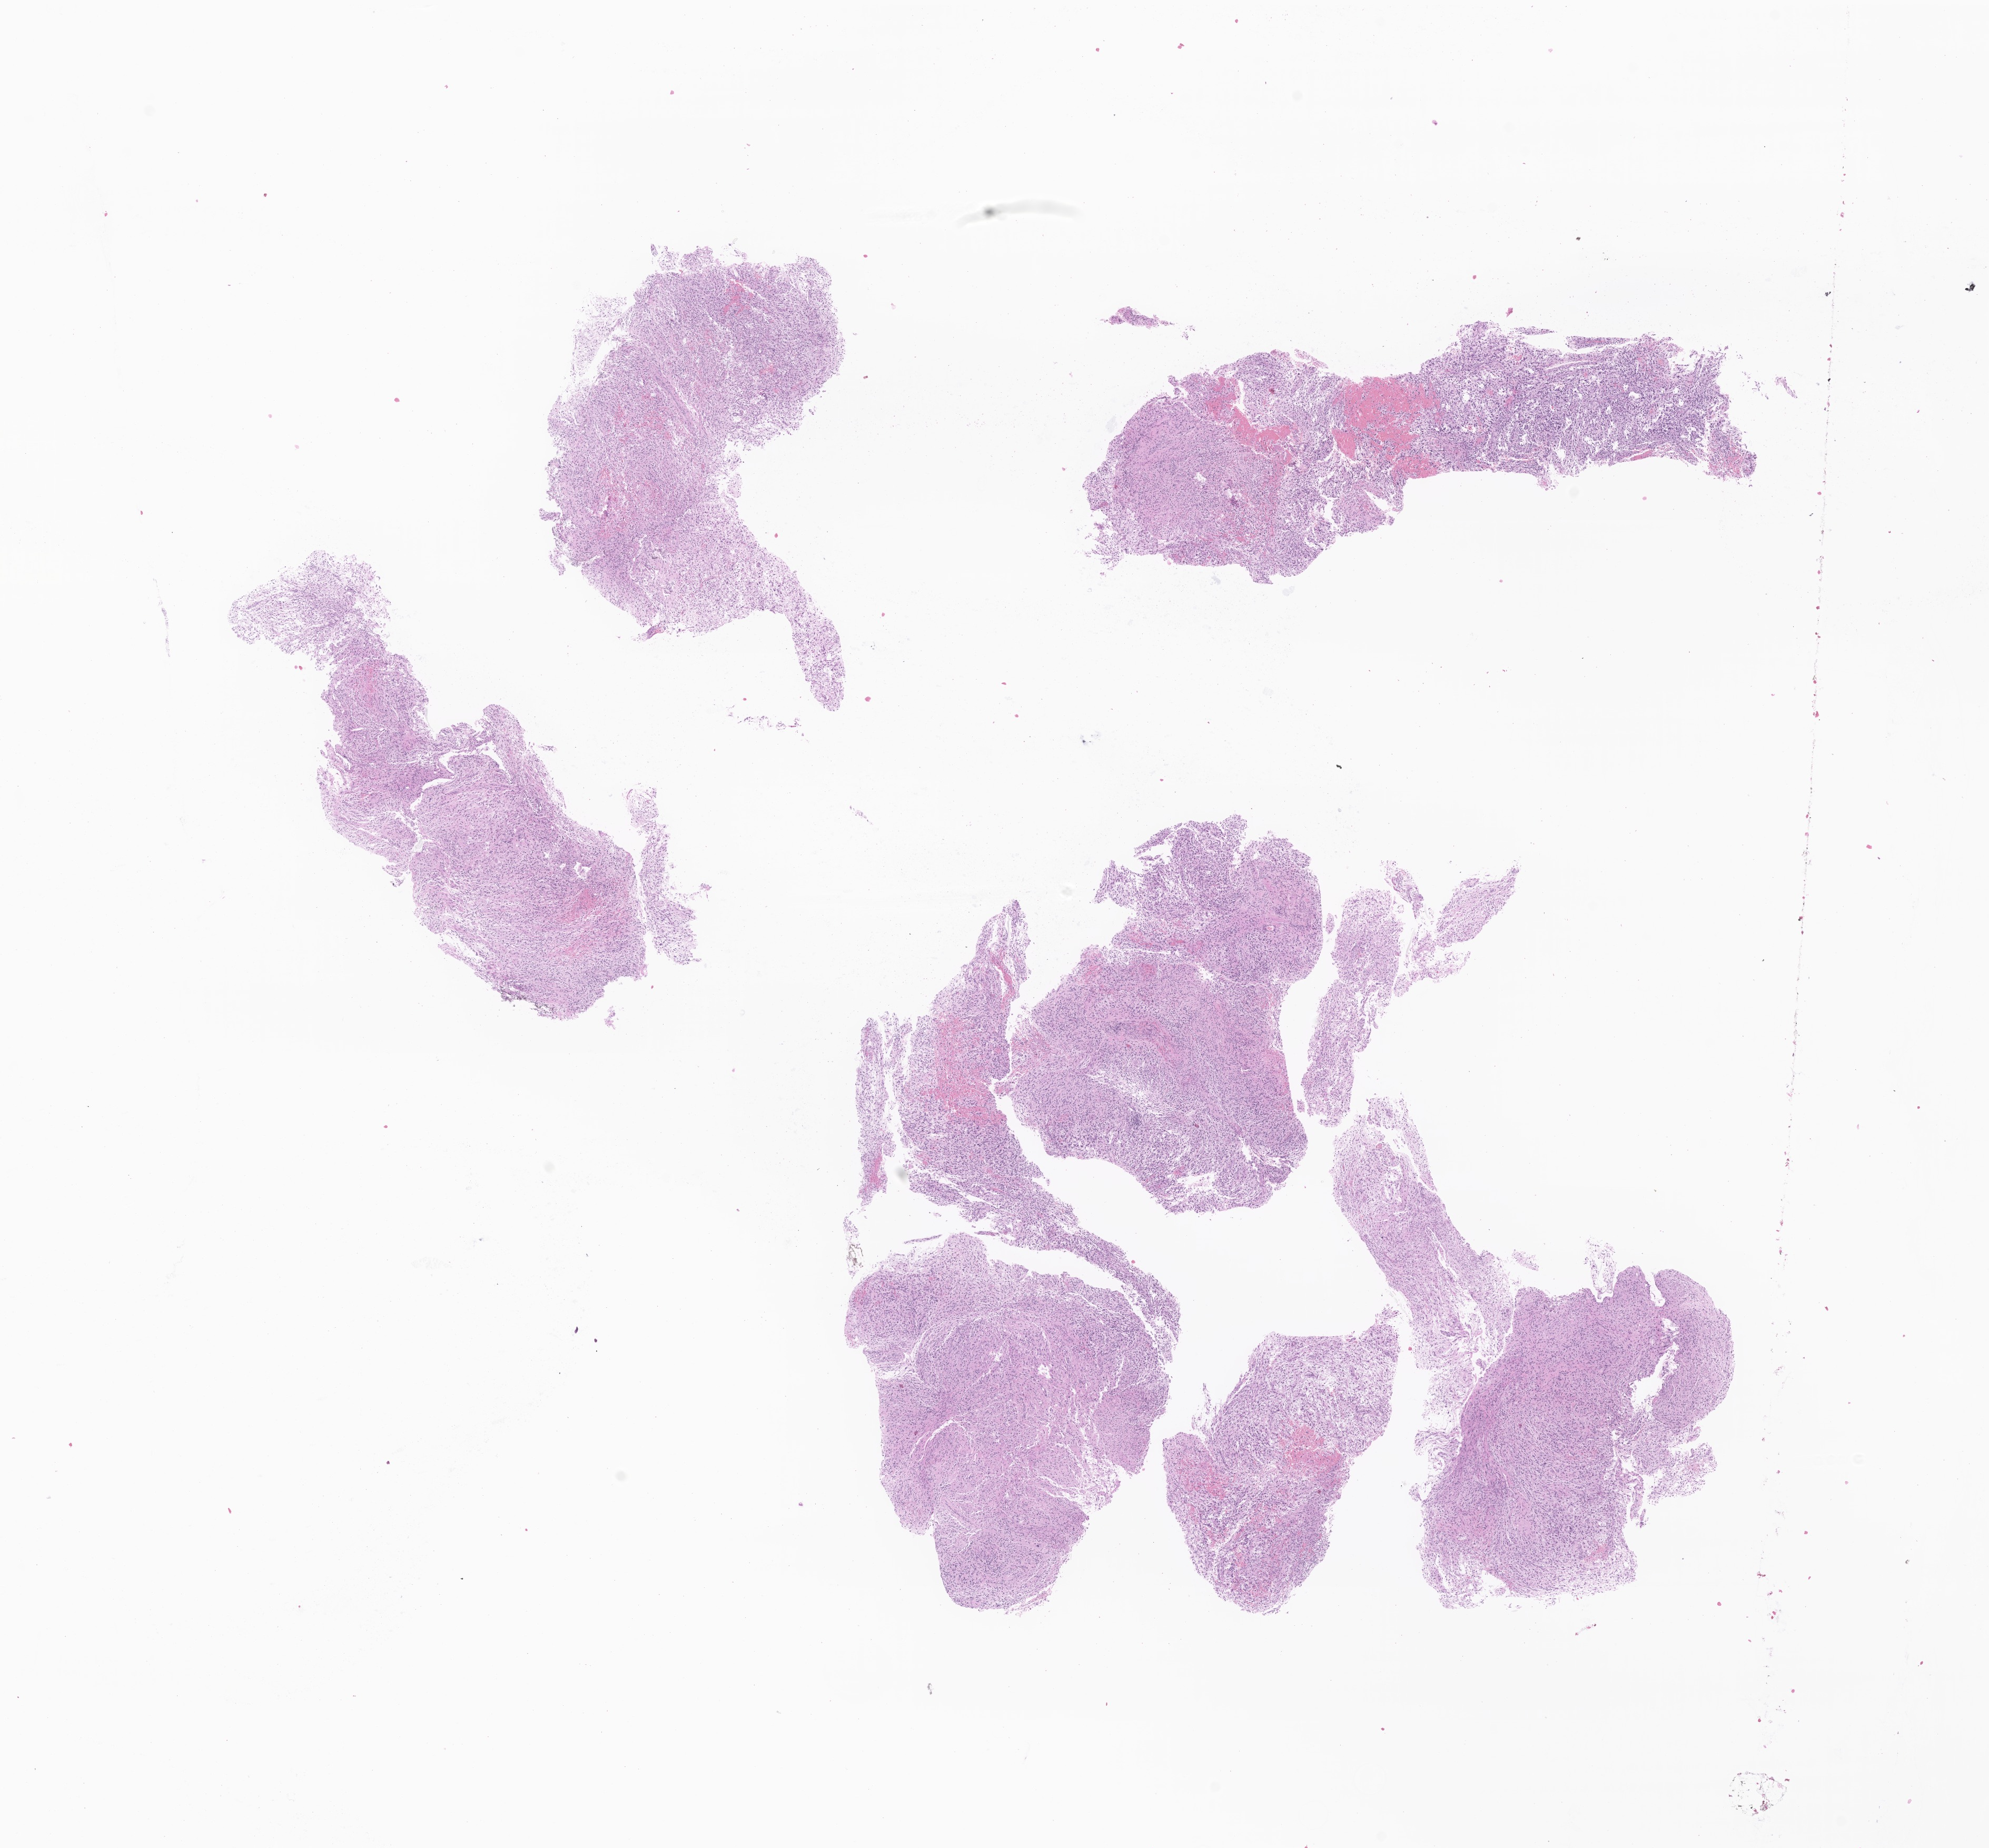
Whole-slide image, hematoxylin and eosin (H&E) stain of tumor tissue from the brain, a low-resolution overview of the entire scanned area, about 15.9 x 14.8 mm; formalin-fixed paraffin-embedded section. Female patient, age 162 months (13 years 6 months).
Diagnosis (ICD-O-3 morphology term): Astrocytoma, NOS.